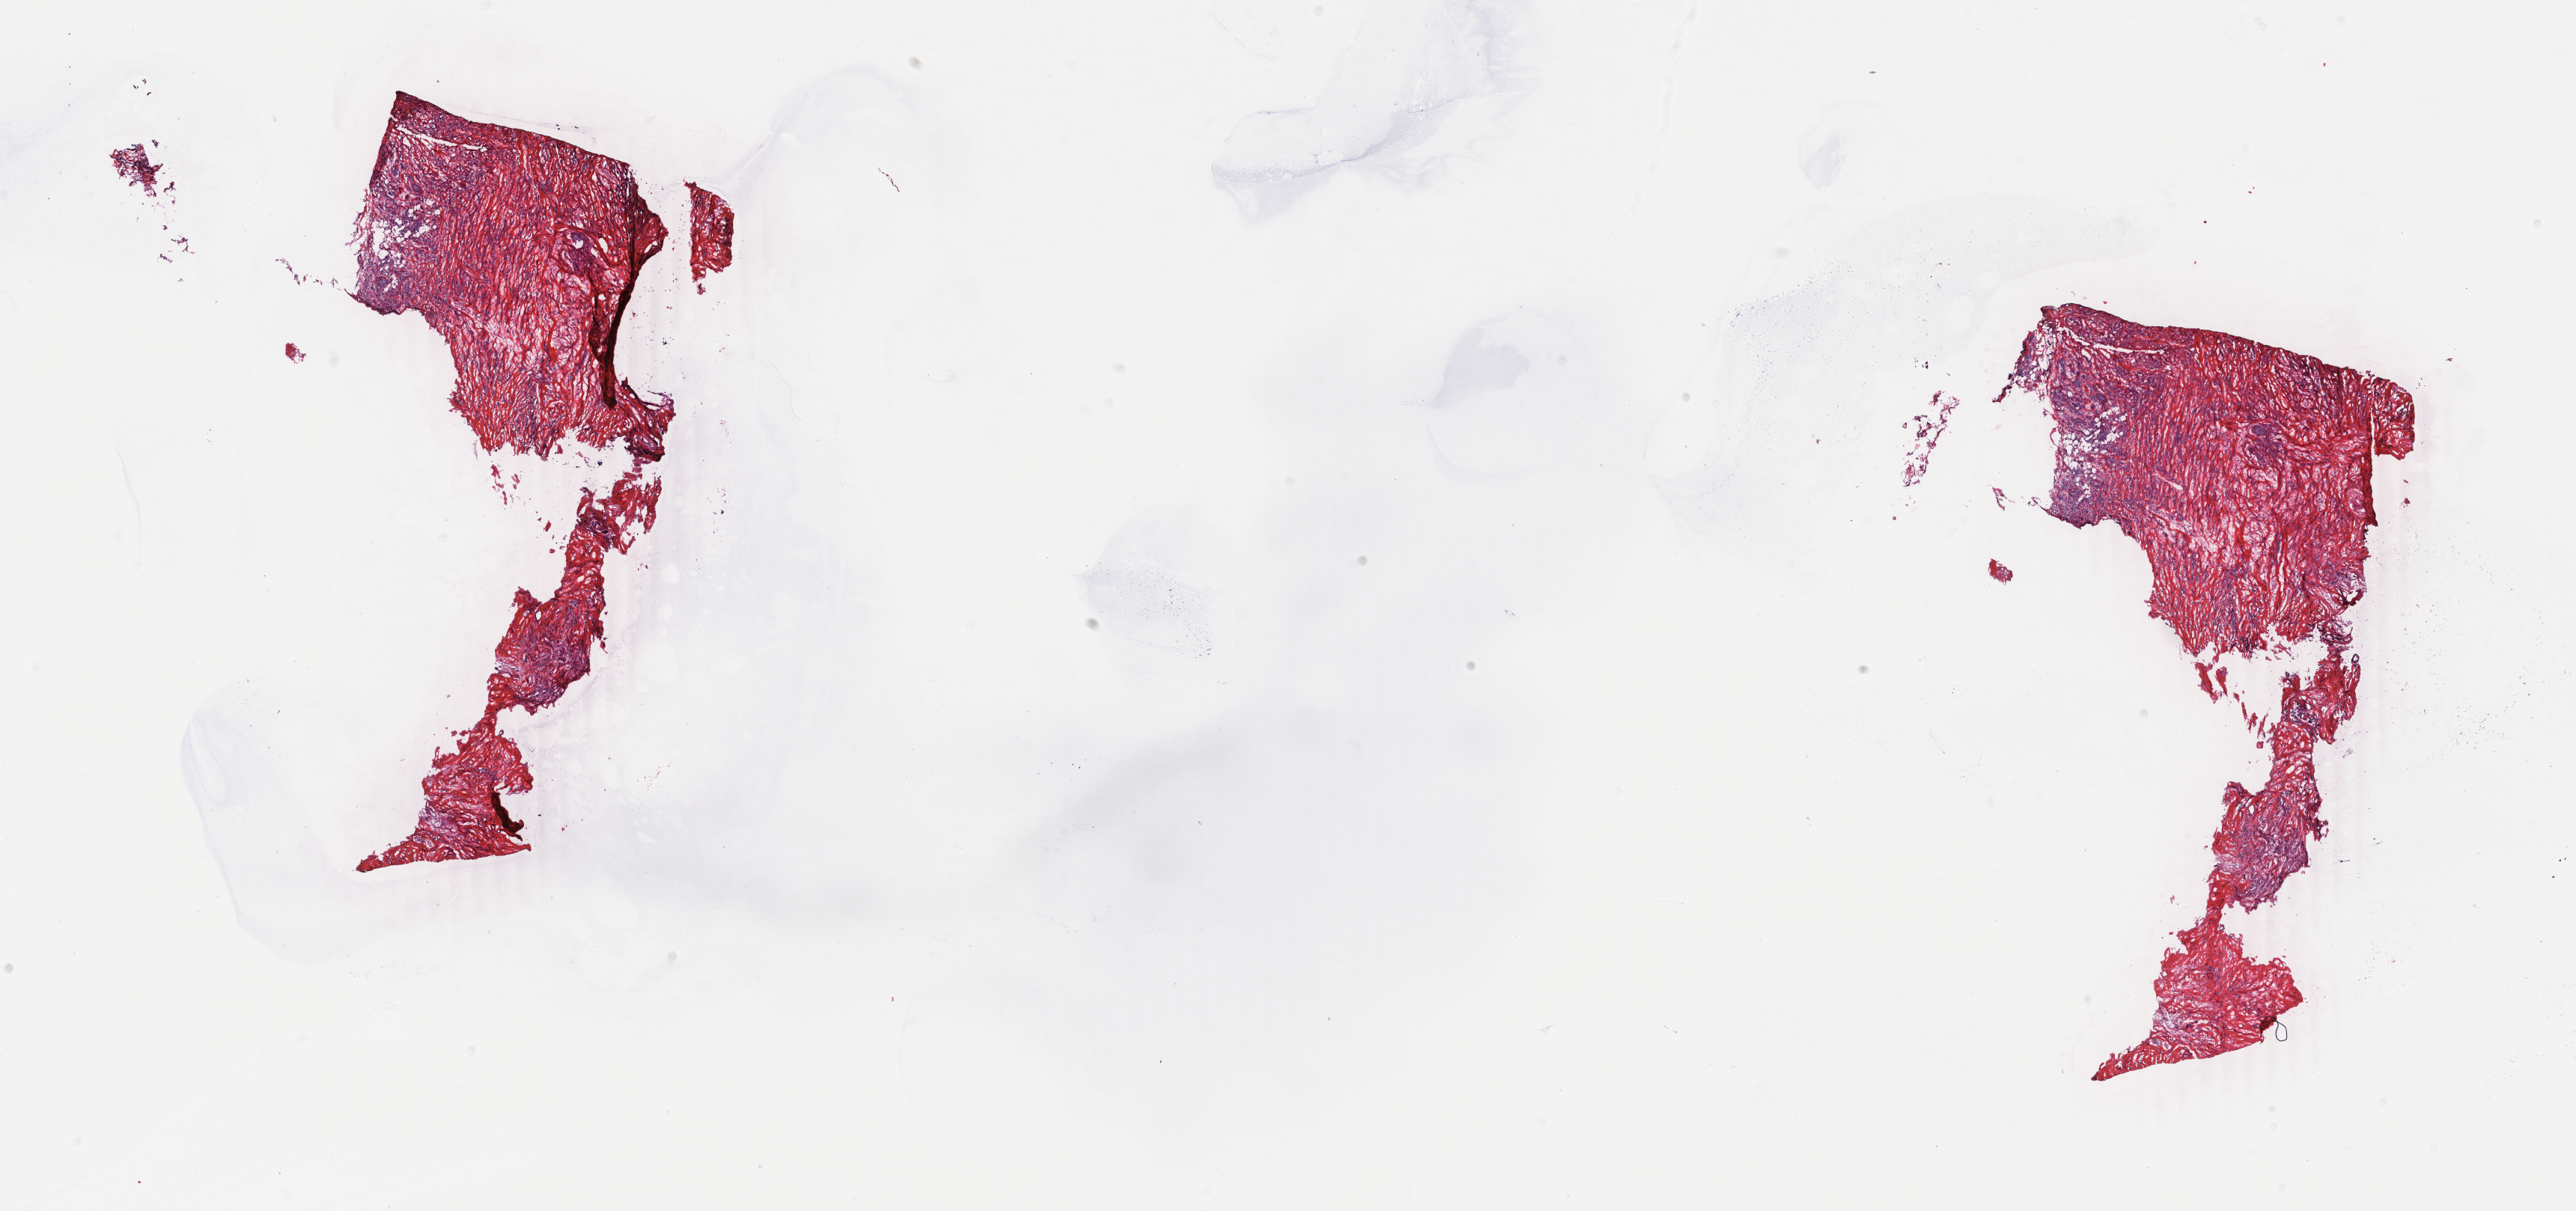
H&E whole-slide image — whole scanned area (about 27.4 x 12.9 mm, from a 40x scan) shown as a low-resolution overview; frozen section; breast, primary tumour sample. Patient: female, age at initial diagnosis 62 years. Composition of this section per pathologist review: tumour cells 80%, tumour nuclei 80%, normal cells 0%, stromal cells 18%, necrosis 2%. Infiltration values recorded for this section: lymphocyte infiltration 3%, monocyte infiltration 0%, neutrophil infiltration 0%.
AJCC pathologic stage: IIIA. TNM: T3 N1 M0. Pathologic diagnosis: Lobular carcinoma, NOS. Lymph nodes positive (case pathology): 1 of 14 examined.